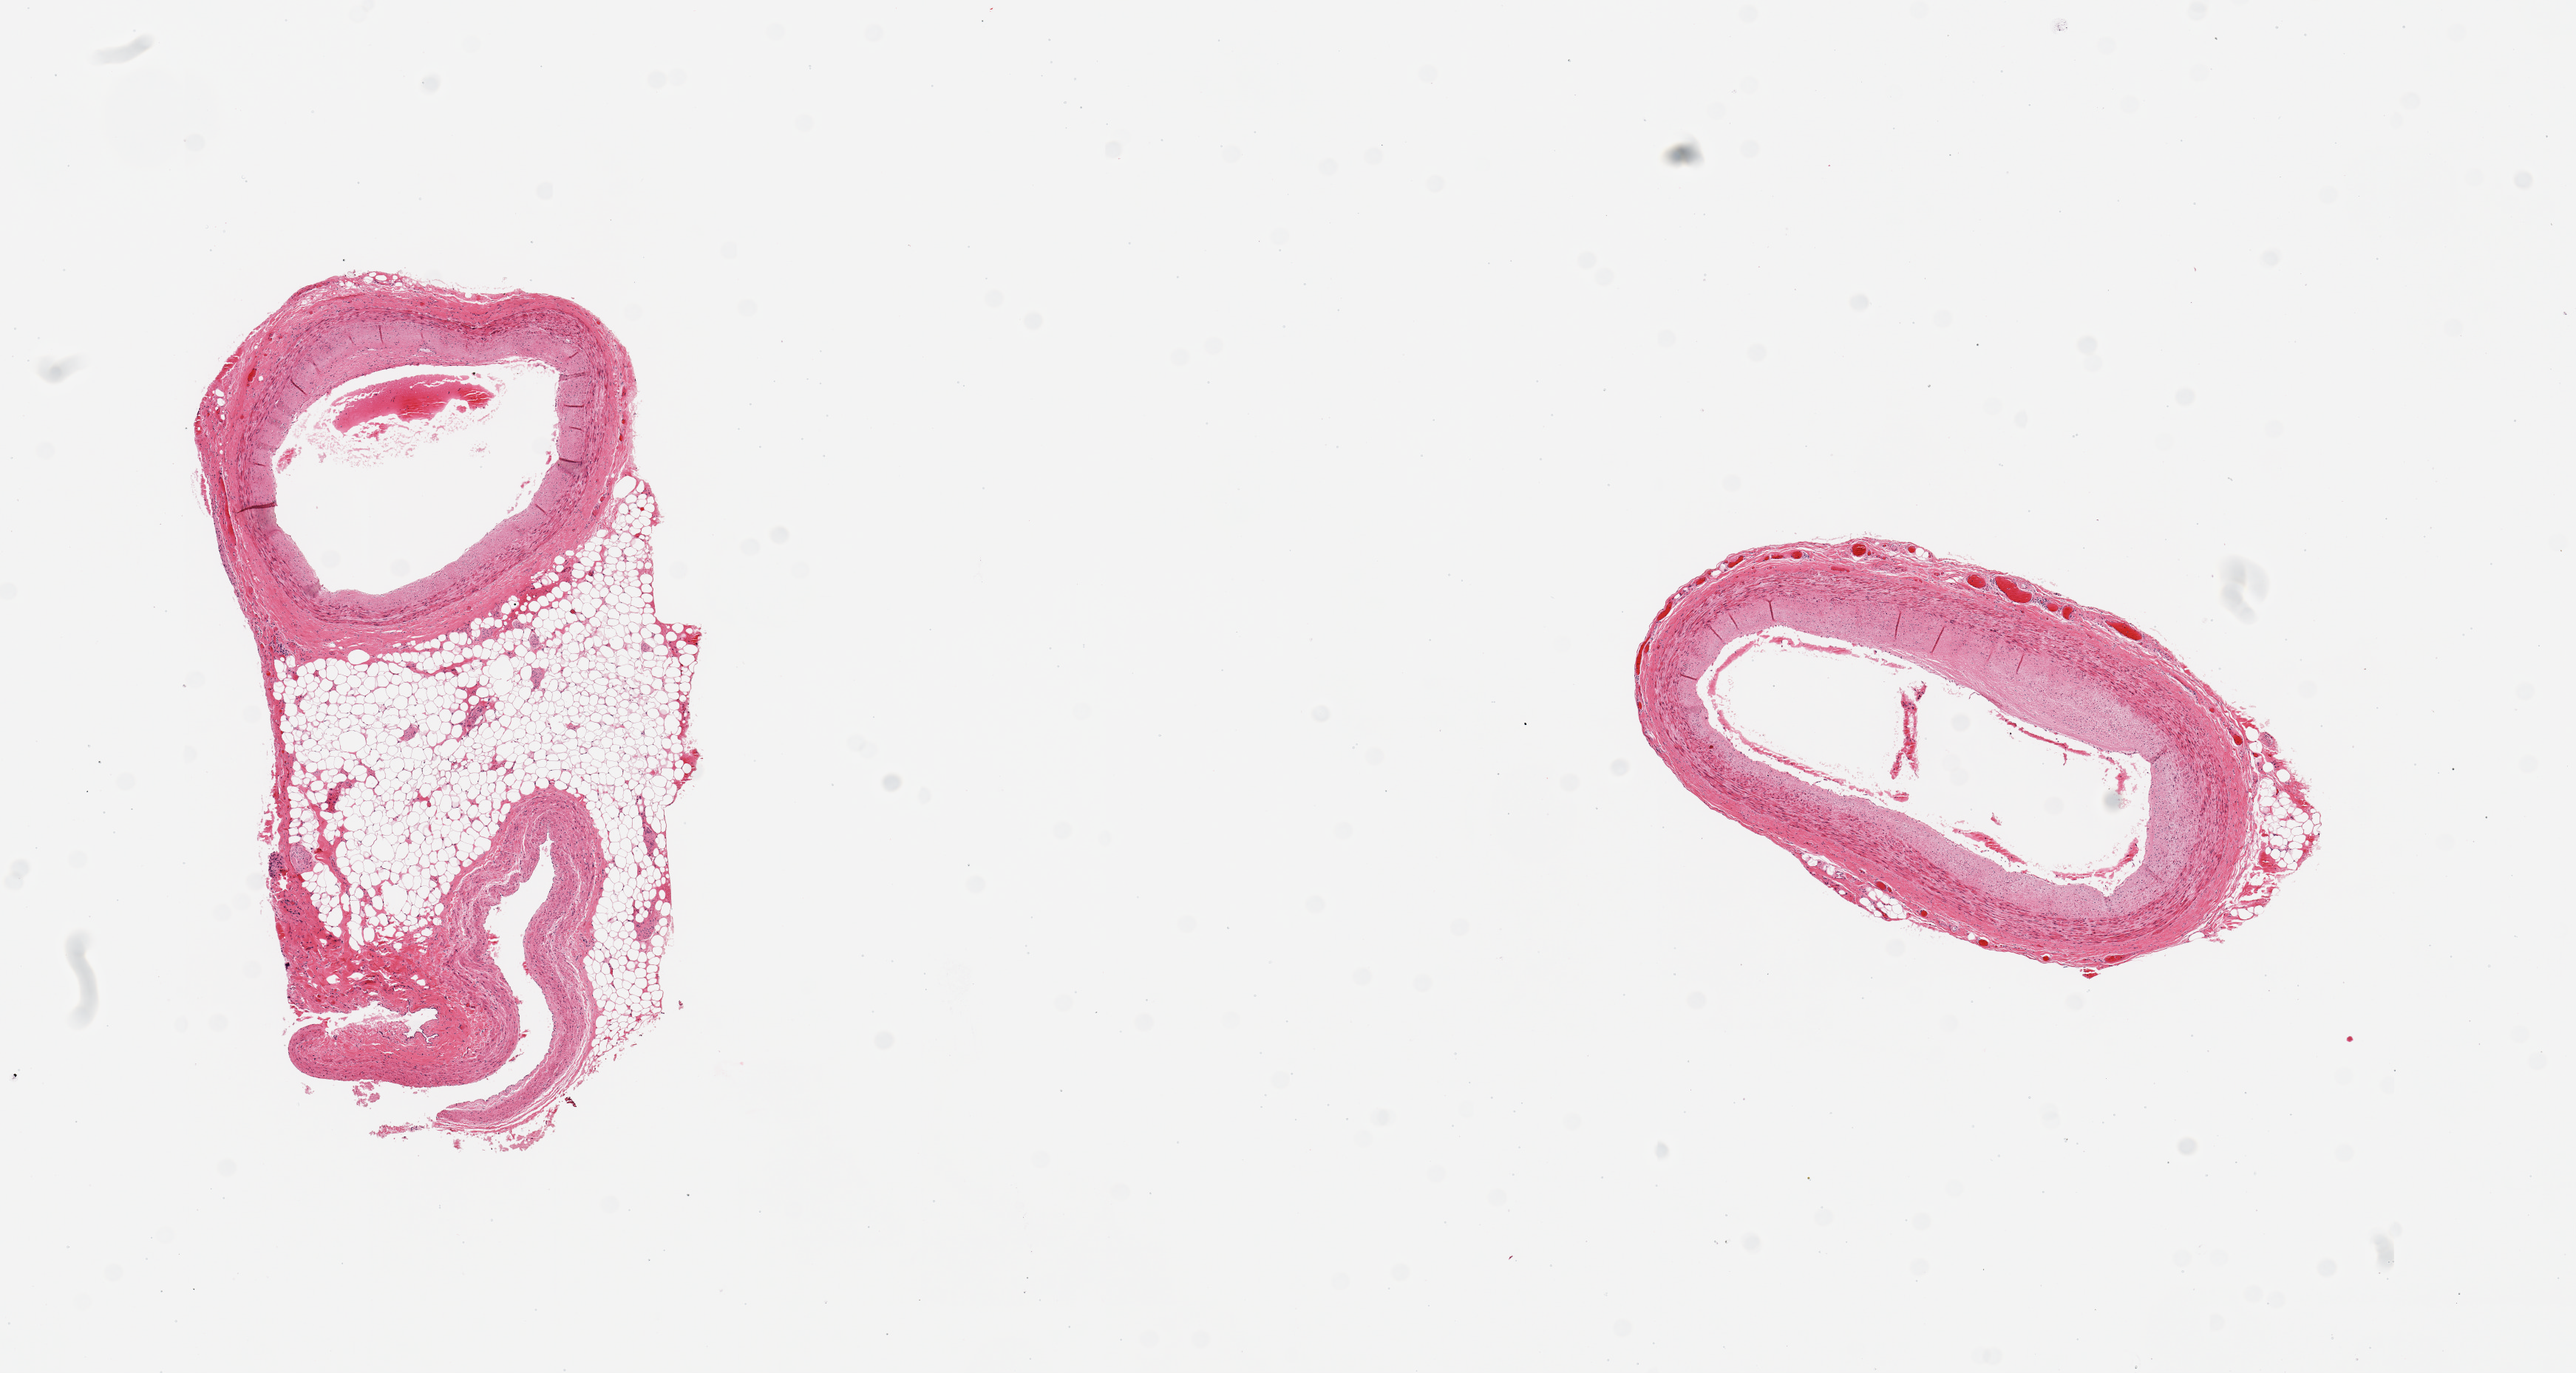
Hematoxylin and eosin (H&E) whole-slide image, brightfield, whole scanned area (about 13.8 x 7.3 mm) shown as a low-resolution overview. PAXgene-fixed paraffin-embedded (PFPE) section. Sampled site (target tissue): coronary artery. Donor tissue sample. Male donor.
- review note (as recorded): 2 pieces, ~10% occlusive atherosis; adherent nubbin fat up to 2mm